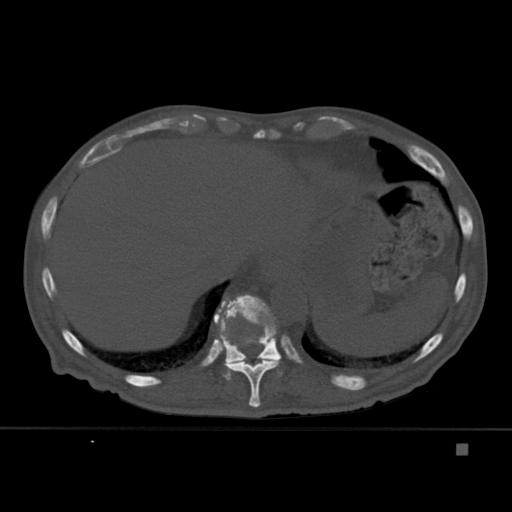
CT including the spine, one axial slice; slice 225 of 451 in the series (ordered by position); bone window (W 1800 / L 400 HU); 1.5 mm slice thickness; 512 × 512 image matrix. Patient: male, 75 years. From the clinical record (not read from this slice): primary cancer: prostate.
Outlined on this slice (semi-automatic segmentation, software-assisted and operator-edited):
- T10 vertebra: bounding box <227,295,283,408> (left, top, right, bottom; pixels)
- T11 vertebra: <213,294,283,380>